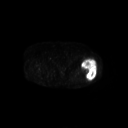
FDG PET of an extremity soft-tissue mass (from a PET/CT study), one axial slice; slice 242 of 267 in the series (ordered by position); 3.27 mm slice thickness; 128 × 128 image matrix. Female patient, age 62 years. Case-level facts recorded for this patient, not image findings: histological type: undifferentiated – high grade; grade: high; site of the primary tumour: left thigh.
Outlined on this slice (expert contour drawn on MRI and transferred to this co-registered scan by the dataset authors):
- gross tumour volume including surrounding oedema: bounding box (x1, y1, x2, y2) in pixels: (81, 59, 97, 81)
- gross tumour volume (mass): (81, 59, 97, 81)